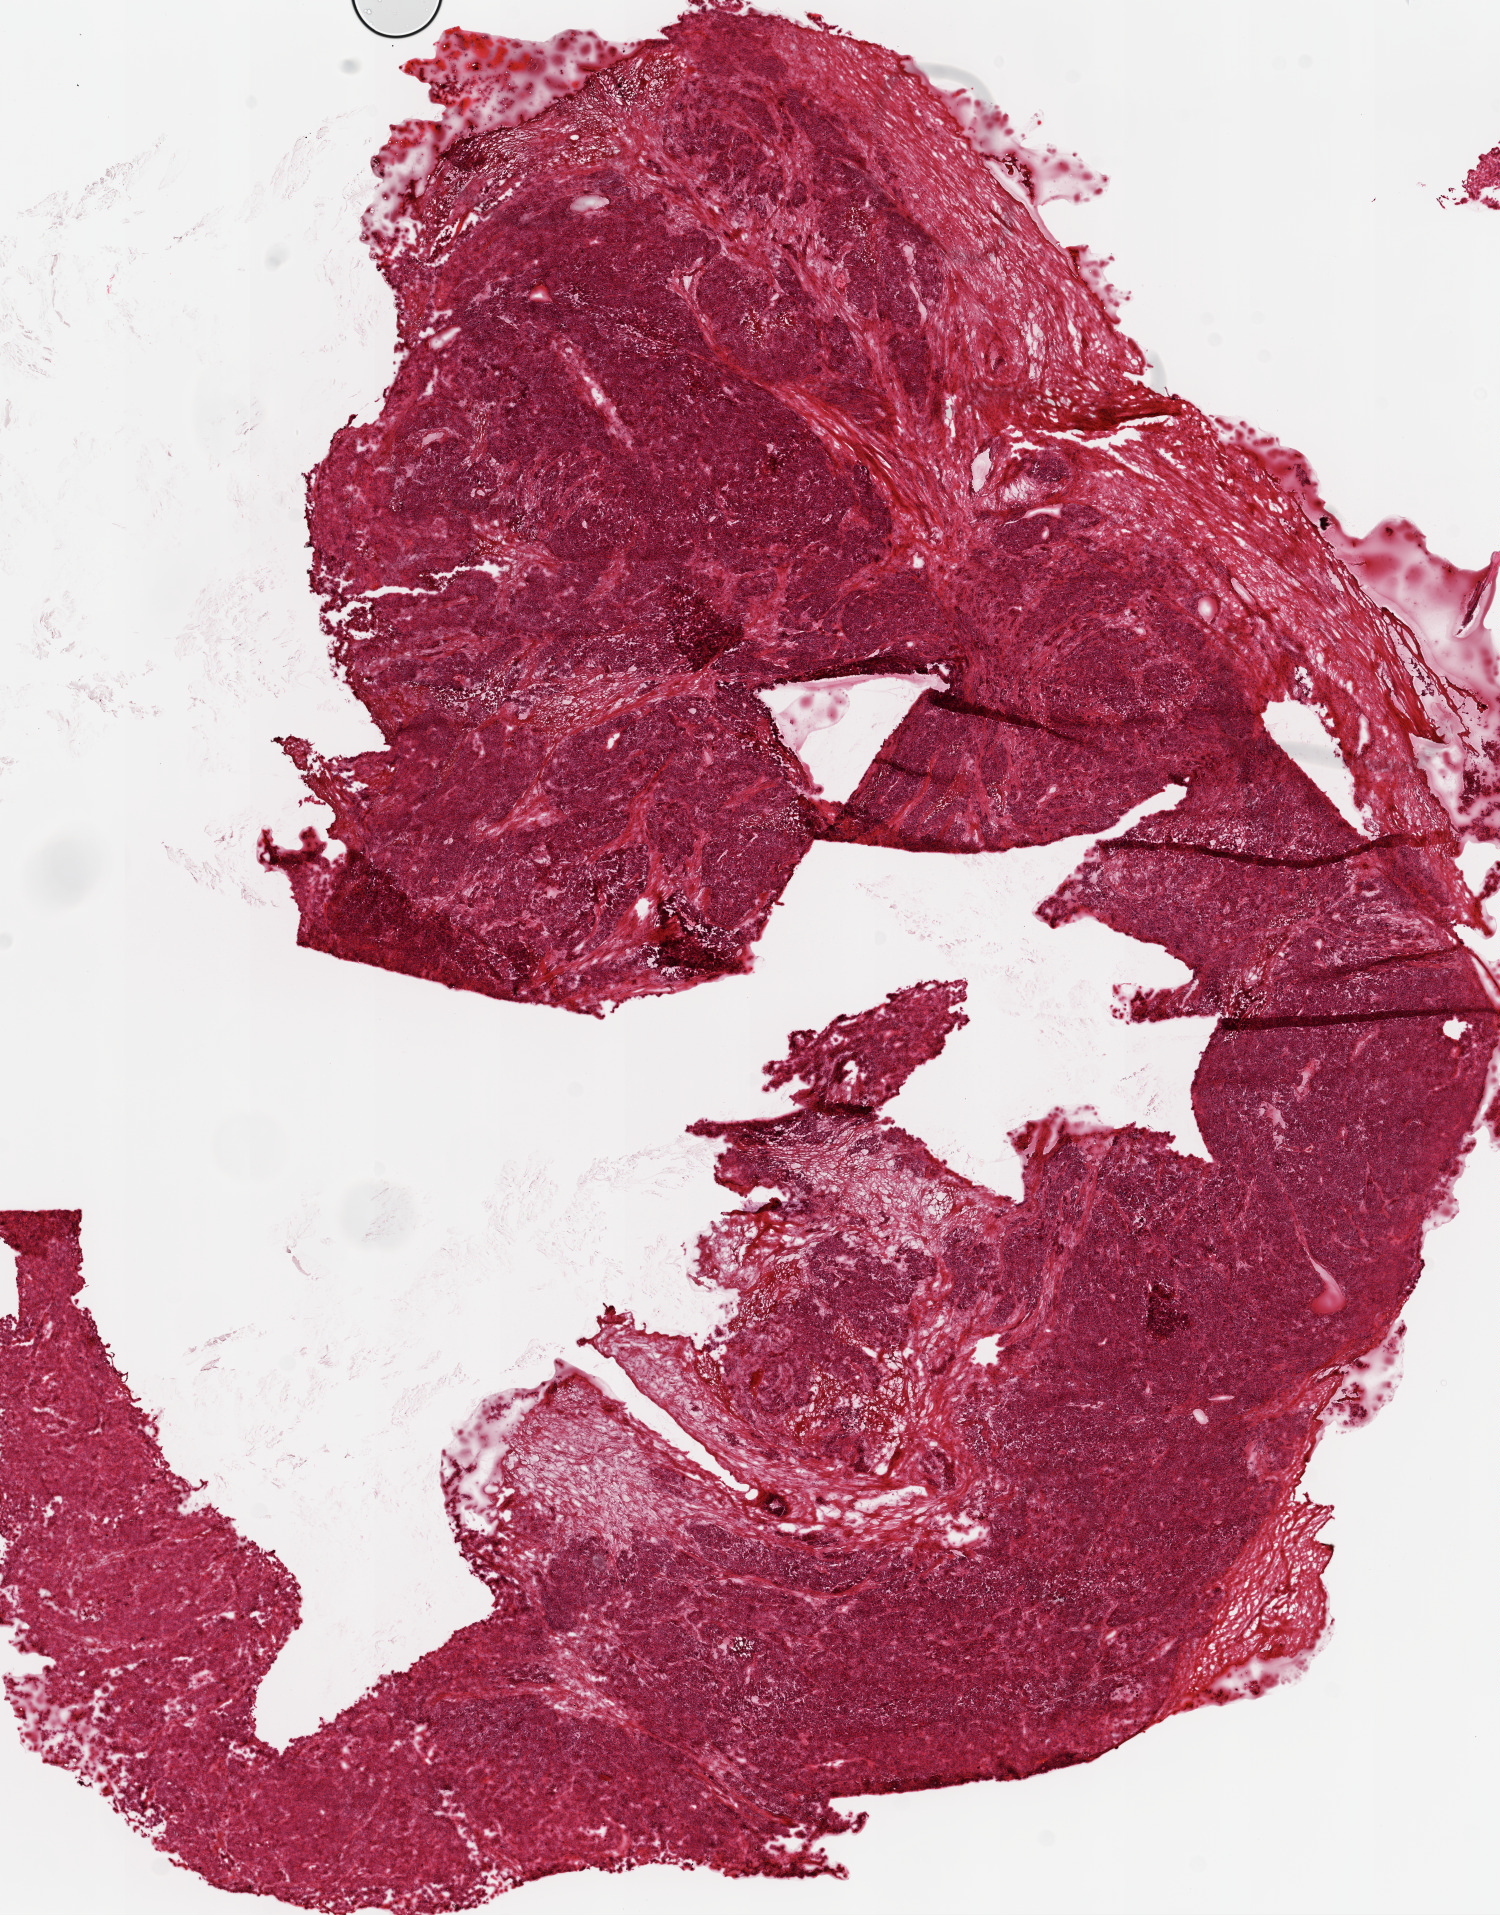
H&E whole-slide image, low-resolution overview of the scanned area, about 12.0 x 15.4 mm (acquisition: 20x scan), frozen section, ovary, primary tumour sample. Patient: female, age at initial diagnosis 50 years. Histologic grade: G3 (poorly differentiated). Pathologist review of this section (percent, as recorded): tumour cells 89%, tumour nuclei 90%, normal cells 0%, stromal cells 10%, necrosis 1%.
Pathologic diagnosis: Serous cystadenocarcinoma, NOS. FIGO stage: IIIC.